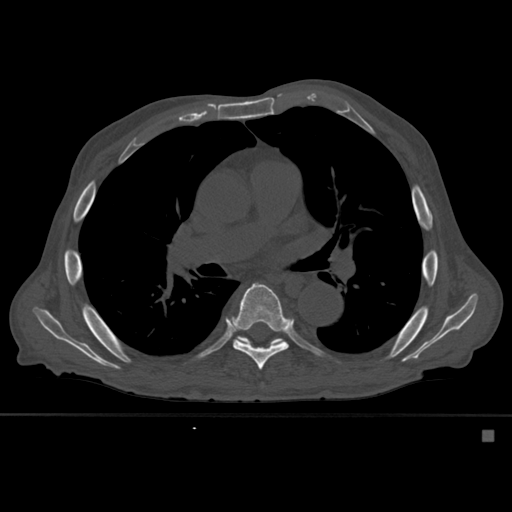
CT including the spine, one axial slice. Position 366 of 527 along the scan axis. Bone window (W 1800 / L 400 HU). 1.5 mm slice thickness. 512 × 512 image matrix, field of view 373 × 373 mm. Patient: male, 78 years. From the clinical record (not read from this slice): primary cancer: prostate.
Outlined on this slice (semi-automatically segmented with operator editing):
- T7 vertebra: bounding box <230,283,290,371> (left, top, right, bottom; pixels)
- T8 vertebra: <238,337,283,346>